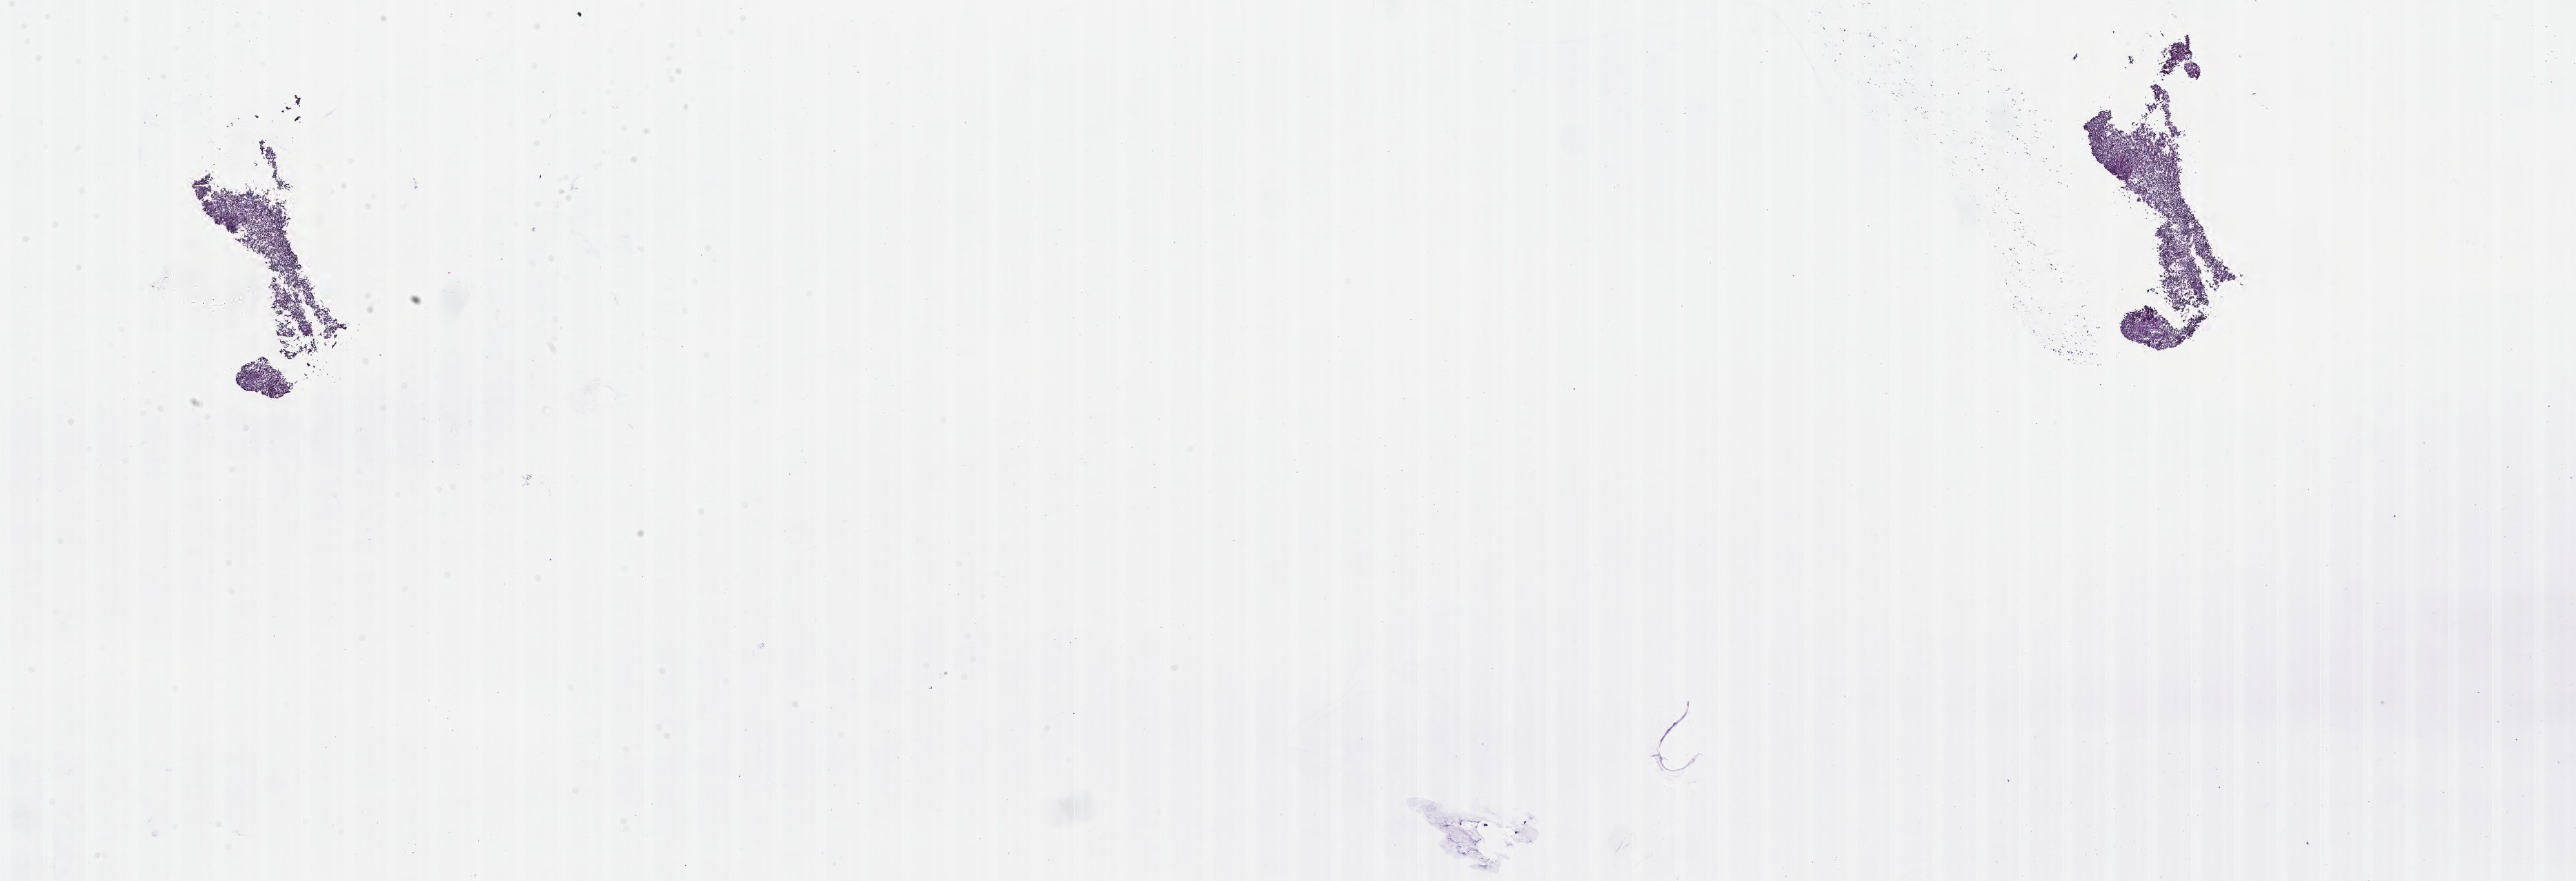
Whole-slide image, haematoxylin and eosin stain of tumor tissue from the brain, whole scanned area (about 30.2 x 10.3 mm) shown as a low-resolution overview; frozen section. Female patient, age 67 months.
Diagnosis (ICD-O-3 morphology term): Medulloblastoma, NOS.